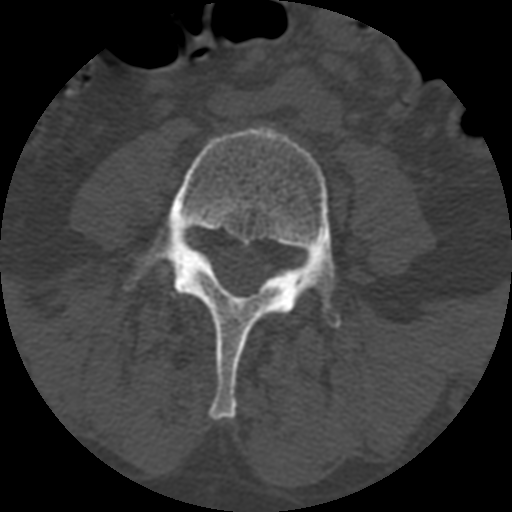
CT including the spine, one axial slice; position 280 of 399 along the scan axis; reconstruction kernel STANDARD; bone window (W 1800 / L 400 HU); 1.25 mm slice thickness; 512 × 512 image matrix, field of view 160 × 160 mm. Patient age 71 years. Case-level facts recorded for this patient, not image findings: primary cancer: prostate.
Outlined on this slice (semi-automatic segmentation, software-assisted and operator-edited):
- L4 vertebra: bounding box <136,127,340,420> (left, top, right, bottom; pixels)
- L5 vertebra: <159,266,167,278>